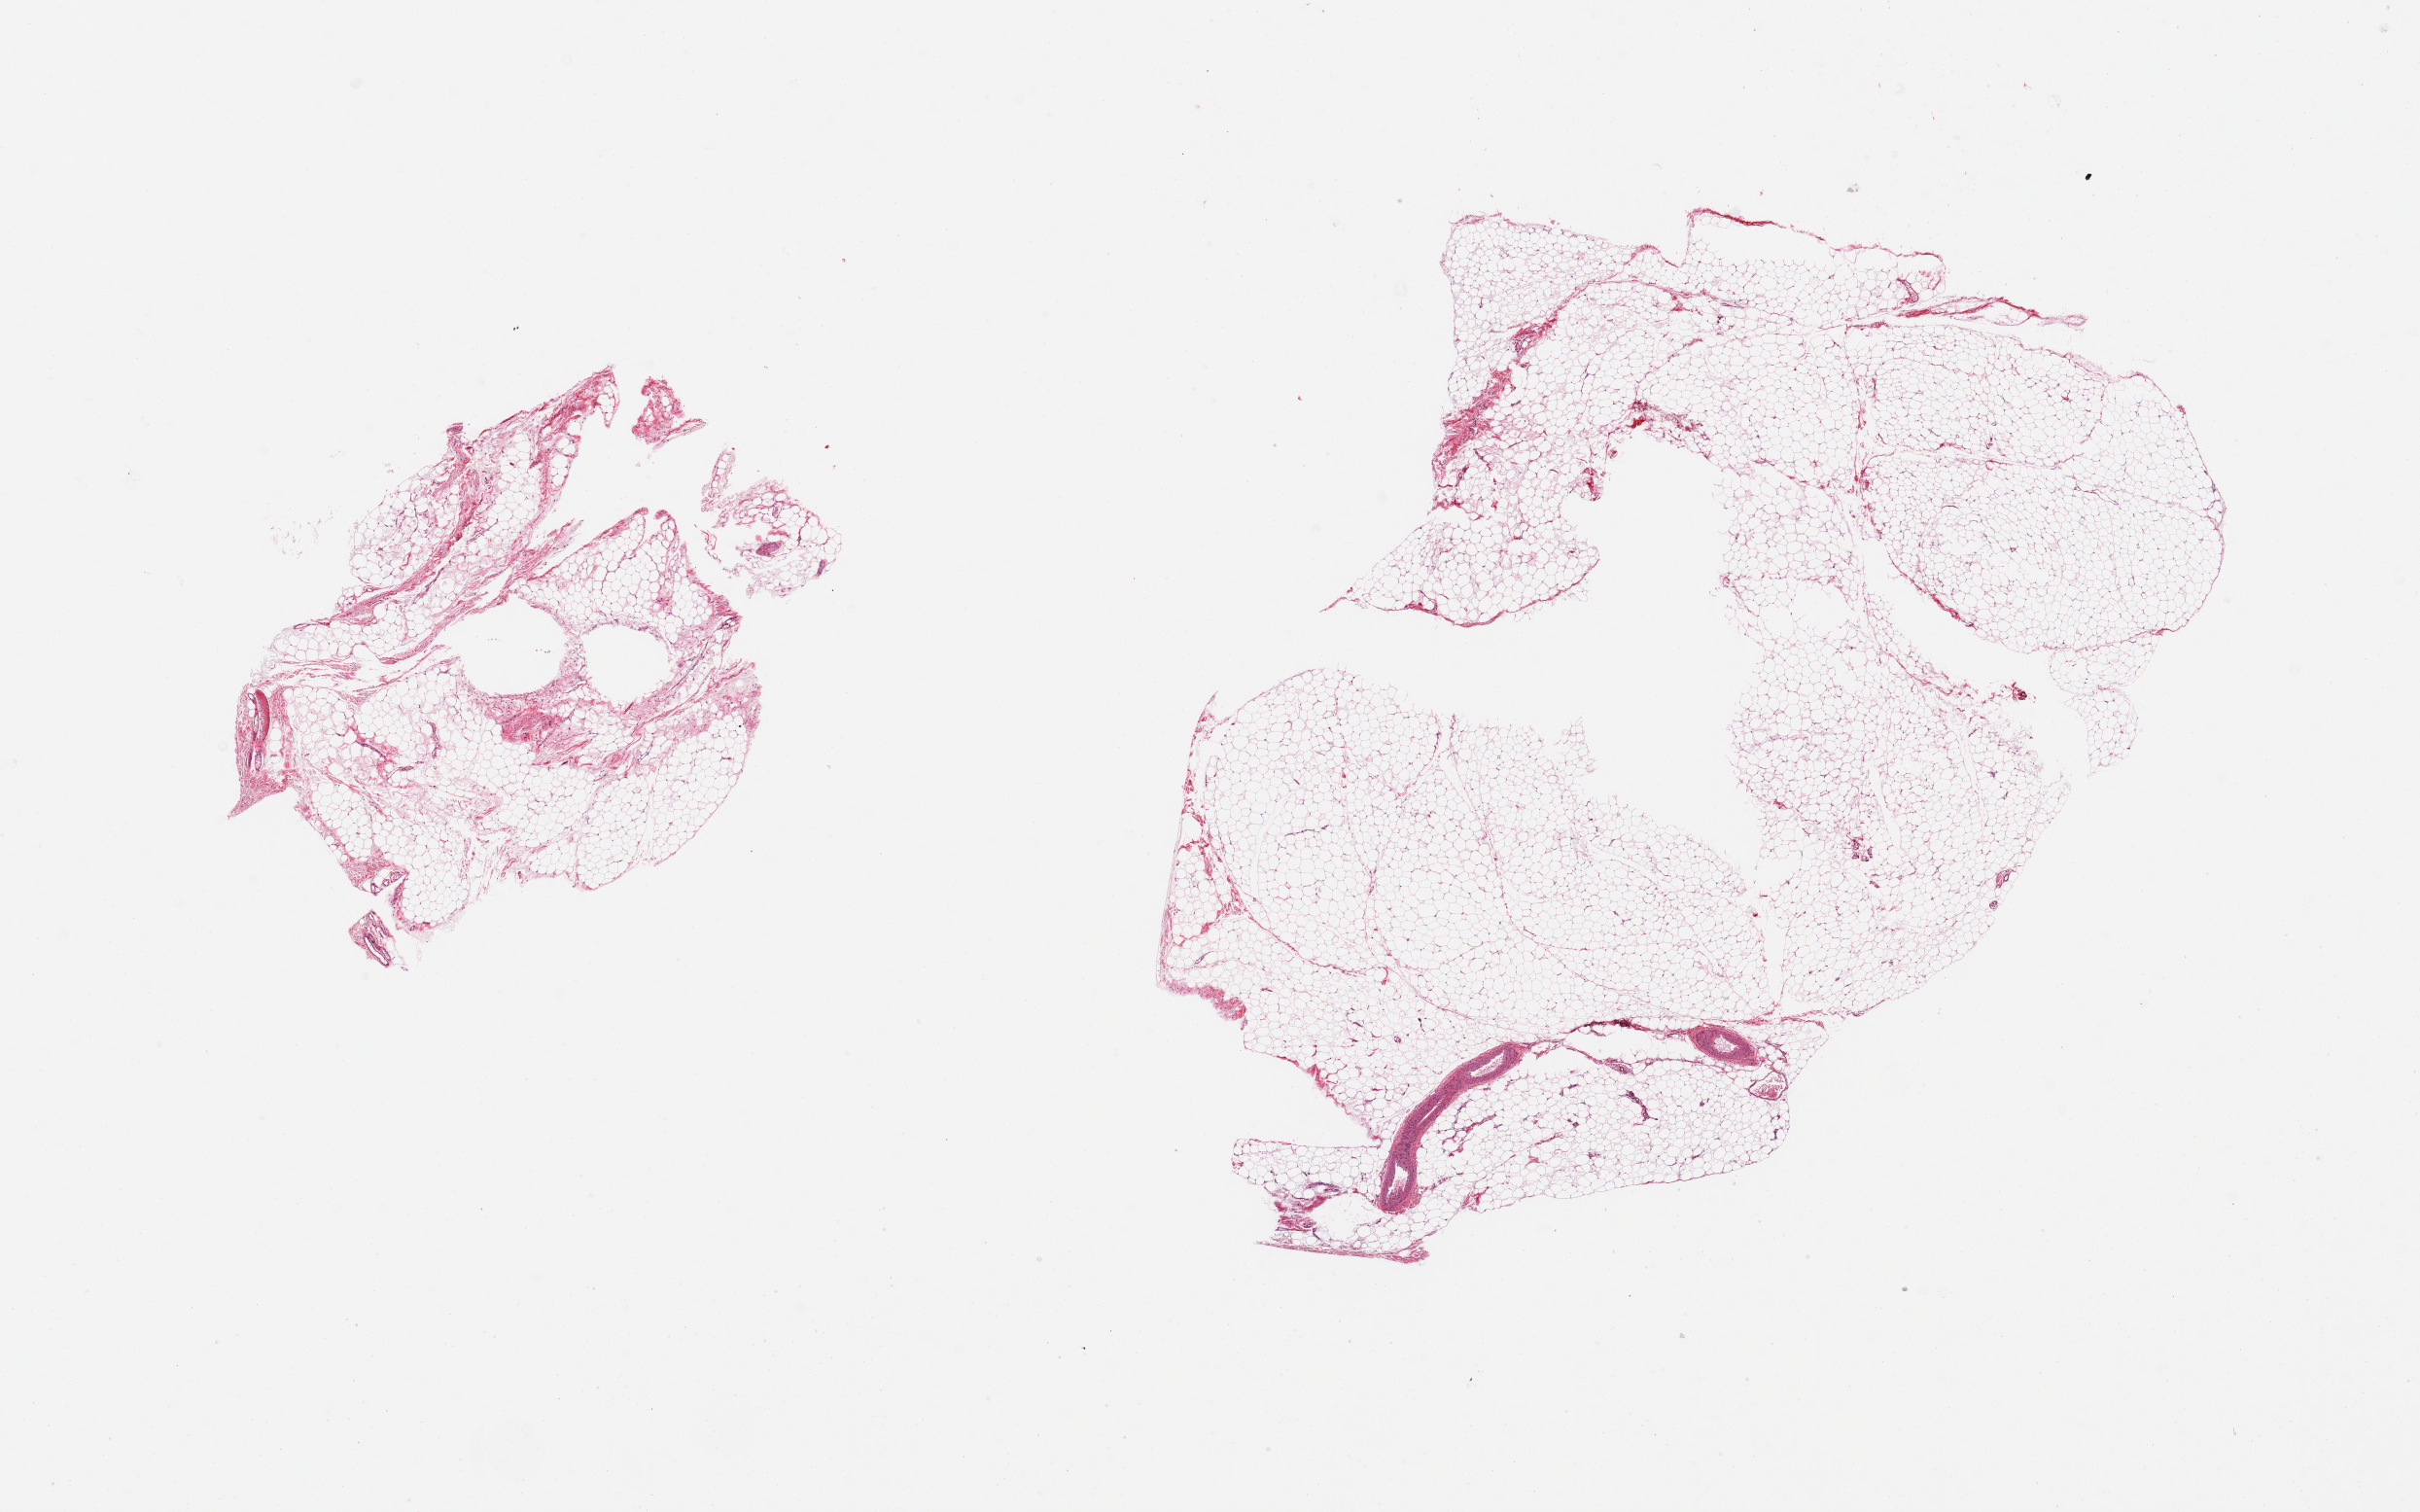
Digitized haematoxylin and eosin-stained section, a low-resolution overview of the entire scanned area, about 19.7 x 12.3 mm, PAXgene-fixed, paraffin-embedded tissue, sampled site (target tissue): omentum, tissue donor sample. Female donor.
- reviewer comment on this tissue sample: 2 pieces; 5% fibrous content